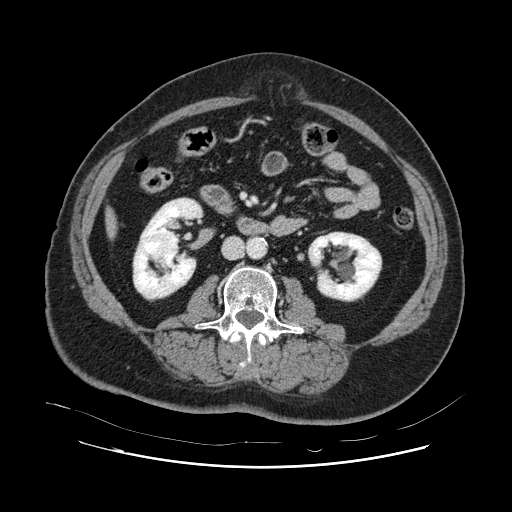
Contrast-enhanced abdominal CT, one axial slice; slice 18 of 132 in the series (ordered by position); intravenous contrast given; soft-tissue window (W 400 / L 40 HU); 512 × 512 image matrix, field of view 391 × 391 mm. Female patient, age 73 years. From the clinical record (not read from this slice): diagnosis: colorectal cancer liver metastases, imaged before liver resection.
Structures marked on this image (manually delineated by an expert):
- liver: bounding box [x1, y1, x2, y2] px = [110, 217, 114, 228]
- planned liver remnant (the part of the liver to remain after resection): [111, 221, 114, 231]